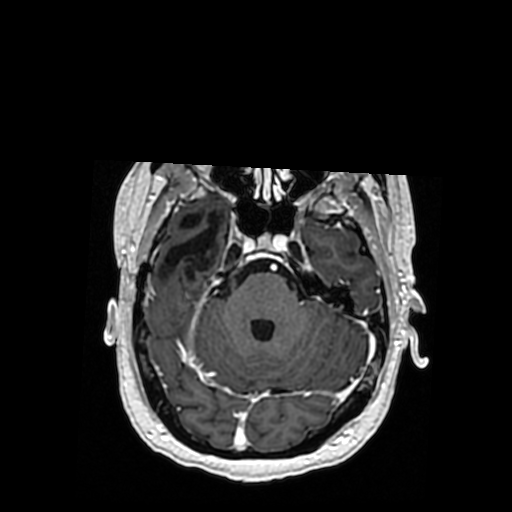
Brain MRI from a brain-tumour surgery series, one axial slice. T1-weighted post-contrast. 0.5 mm slice thickness. 512 × 512 image matrix. From the clinical record (not read from this slice): histopathology: Oligodendroglioma; WHO grade: 3; IDH mutation: yes; tumour location: Right Posterior Temporal Inferior Parietal.
Annotated regions visible in this slice (manually delineated by an expert):
- previous resection cavity: bounding box <160,213,220,278> (left, top, right, bottom; pixels)